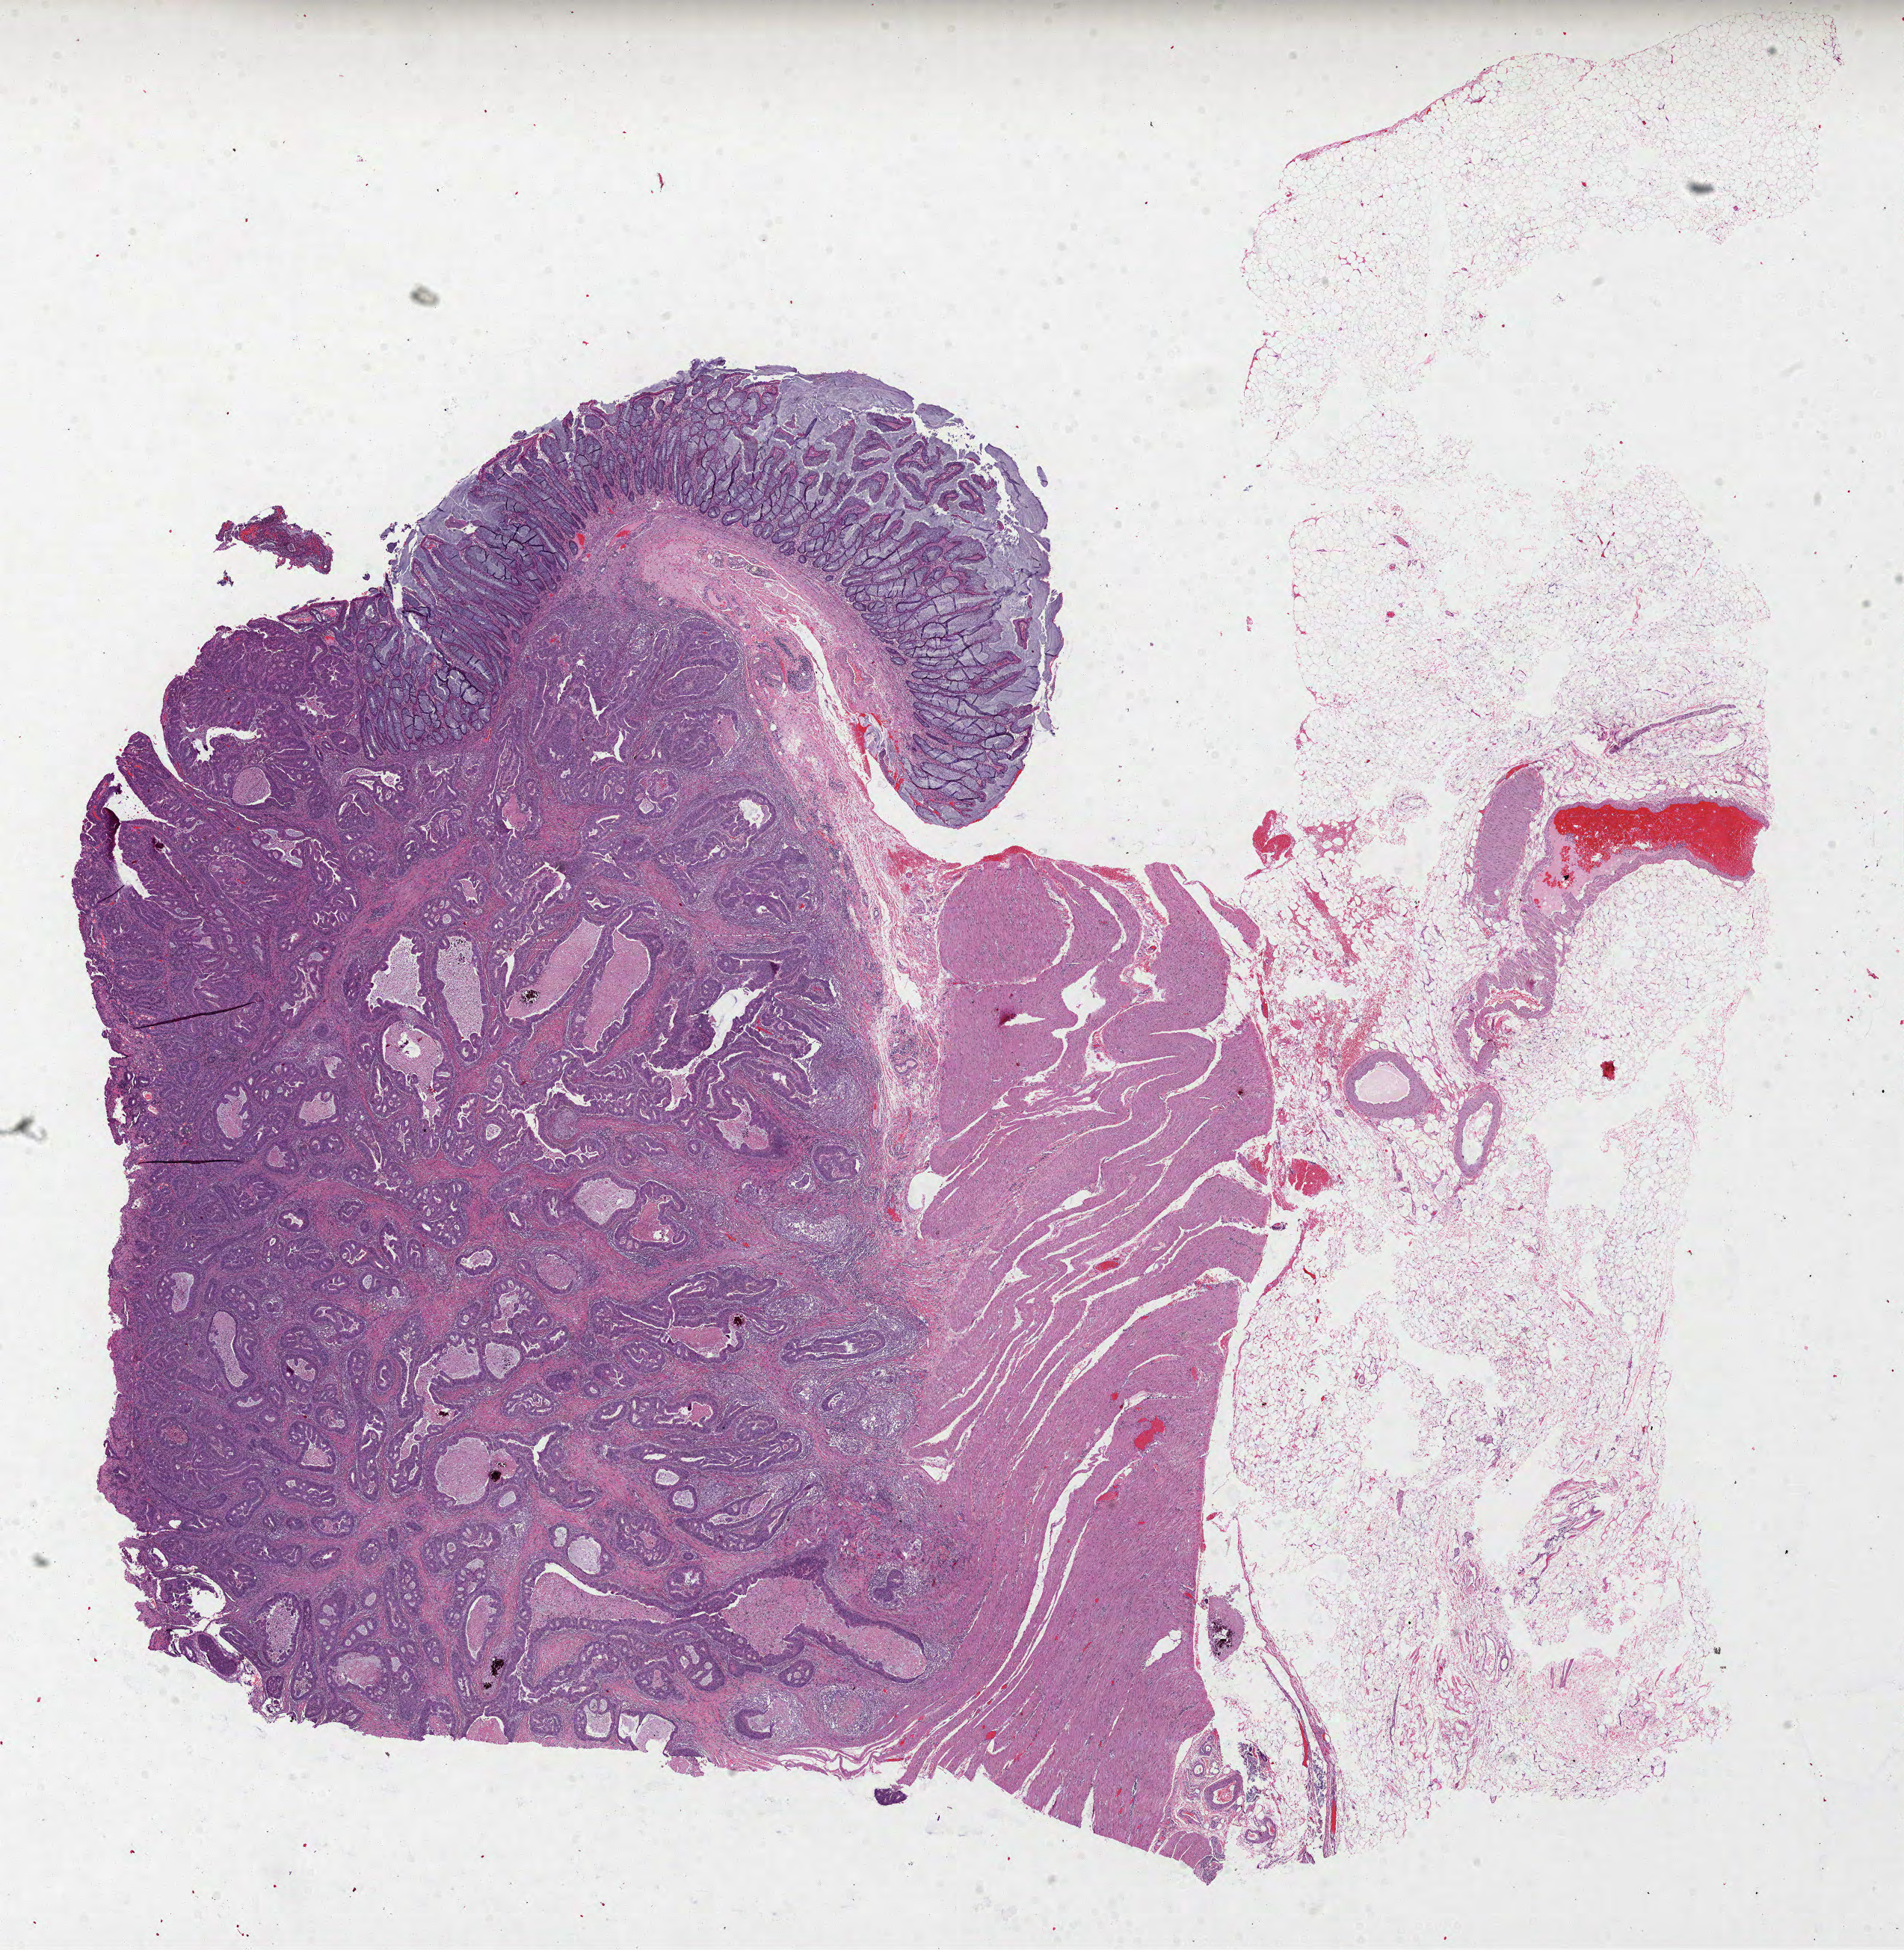
Whole-slide histology image, Hematoxylin and eosin (H&E) stained — a low-resolution overview of the entire scanned area, about 20.5 x 21.0 mm (acquisition: 40x scan), formalin-fixed paraffin-embedded (FFPE) diagnostic section, primary tumour sample from the colon. Patient: female, age at initial diagnosis 82 years.
• AJCC pathologic stage: IIIA
• diagnosis: Adenocarcinoma, NOS (sigmoid colon)